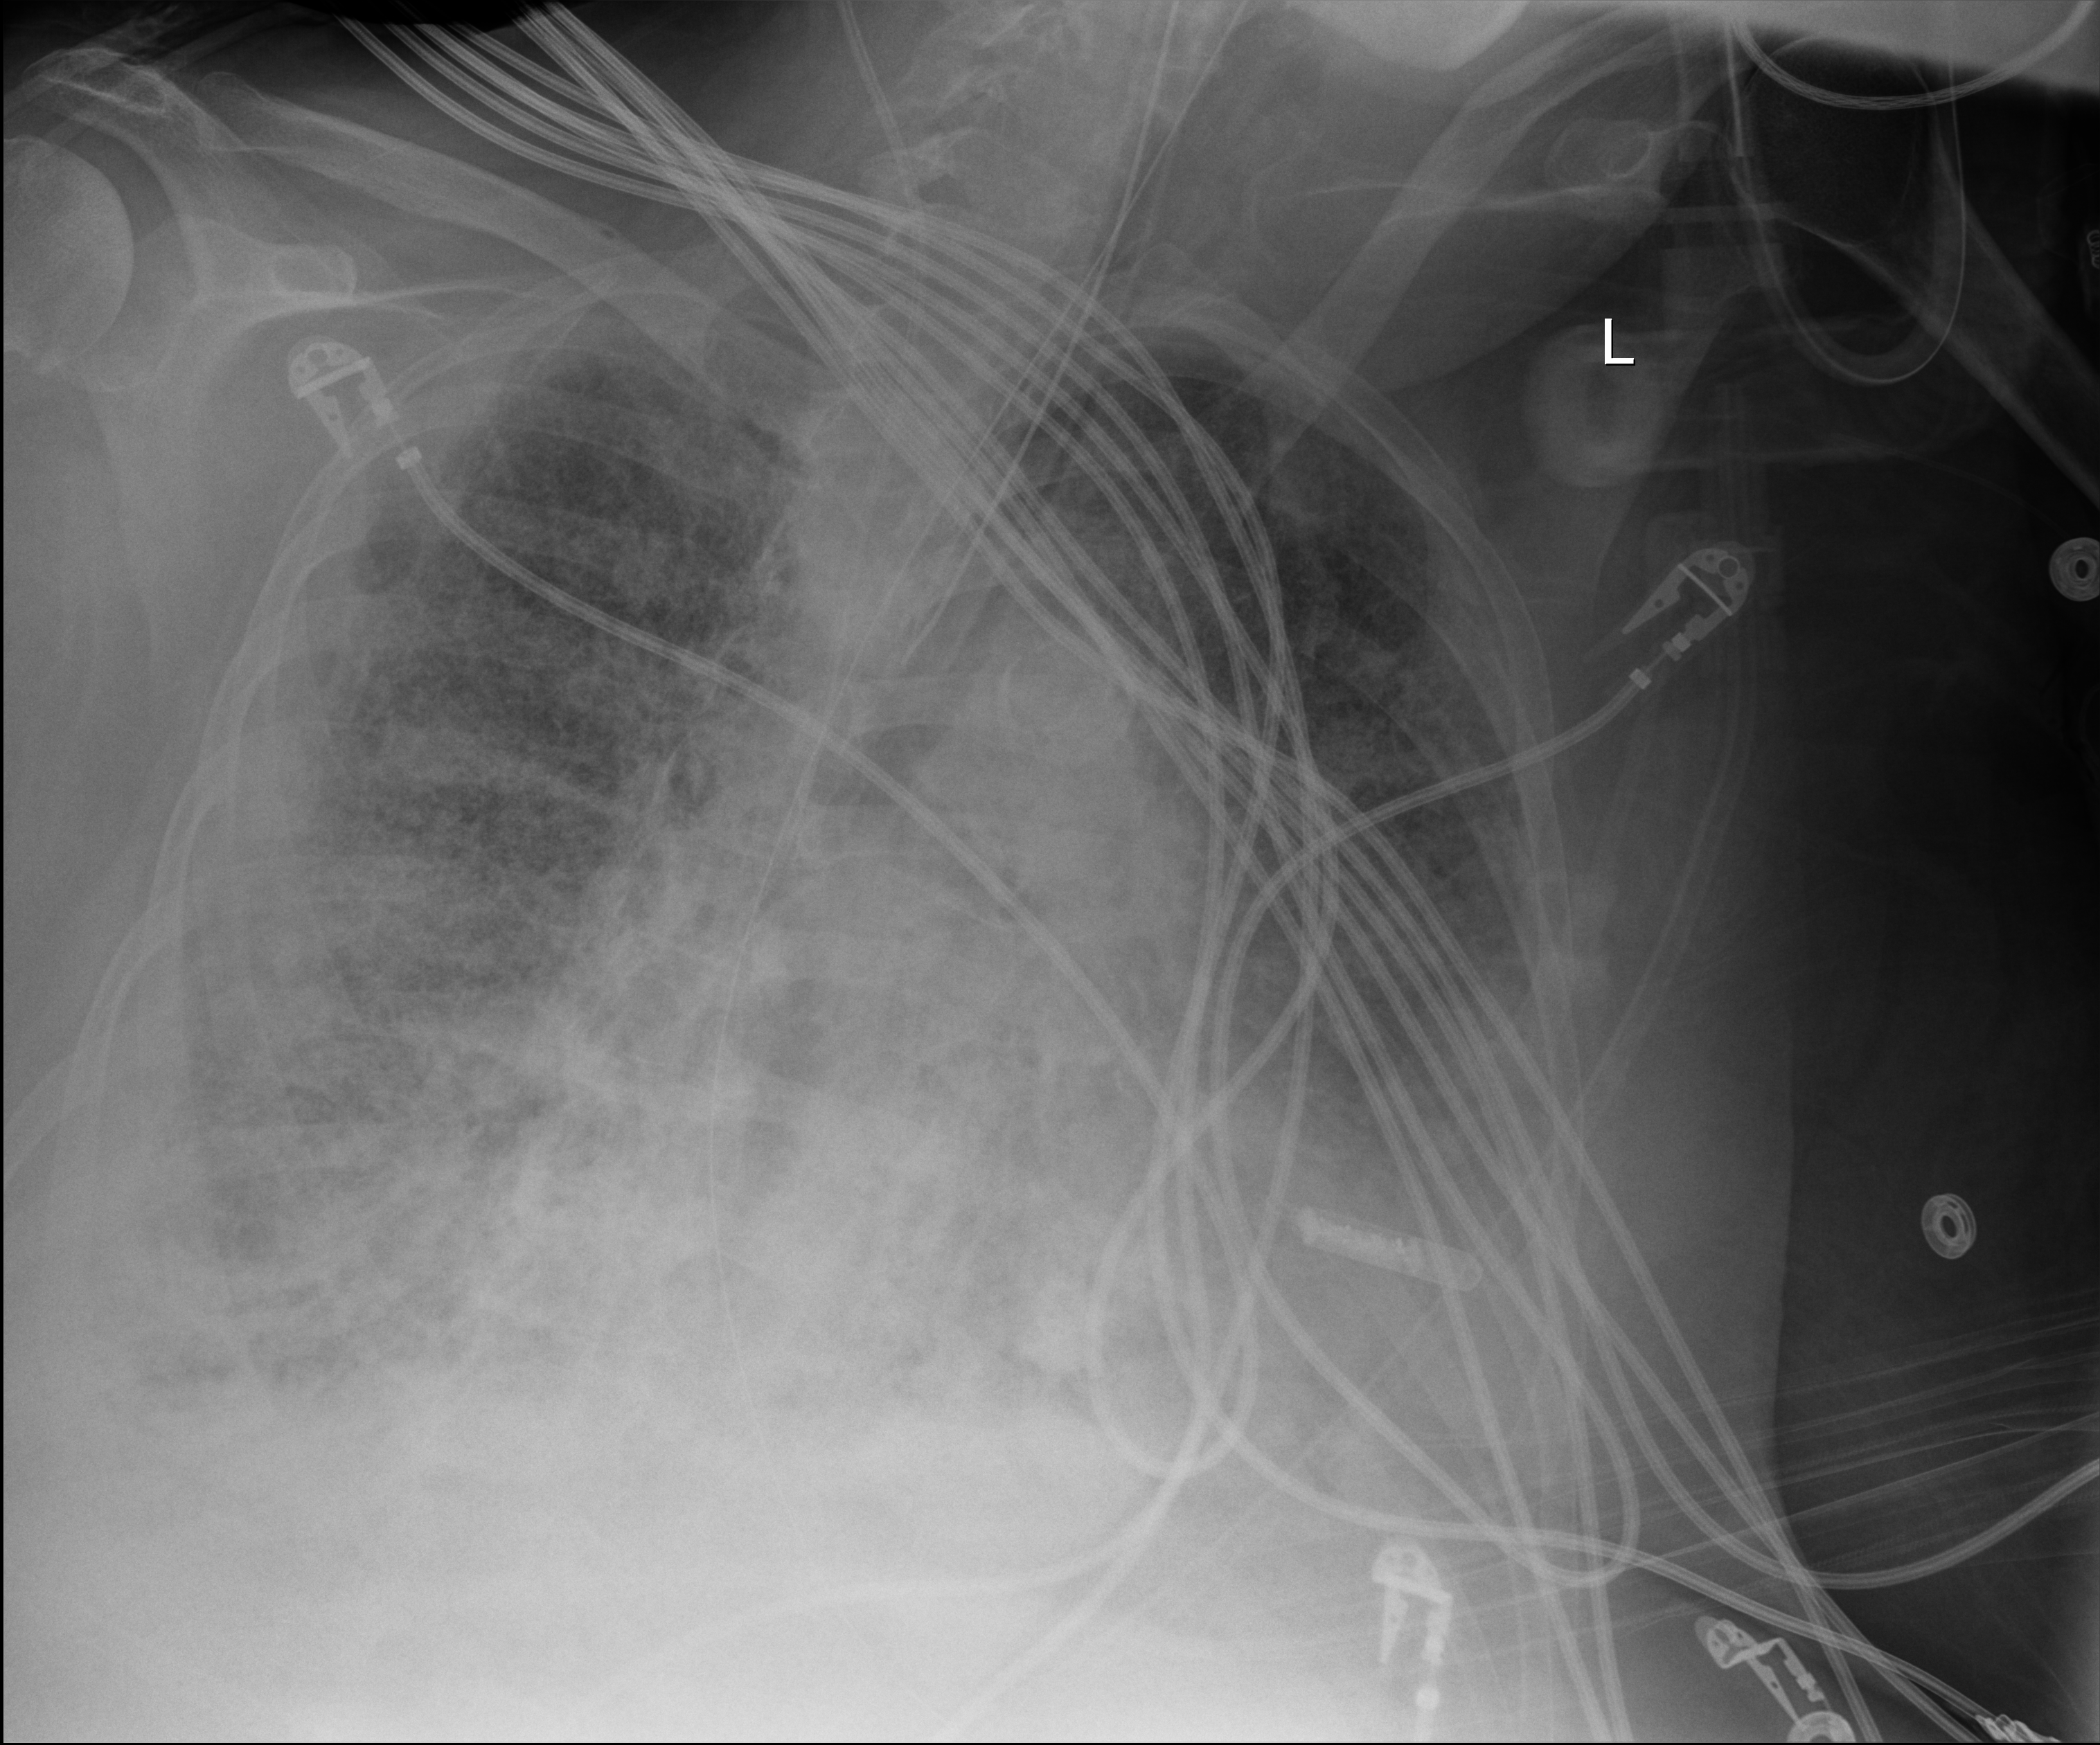
Bedside chest radiograph (digital radiography); anteroposterior (AP) projection. Patient hospitalised with COVID-19; female, aged 60–74 years.
Admission-level facts for this patient (not findings on this image; timing relative to this image not recorded): smoking status (admission record): former; mechanically ventilated during this hospital stay: yes; length of hospital stay: 28 days.